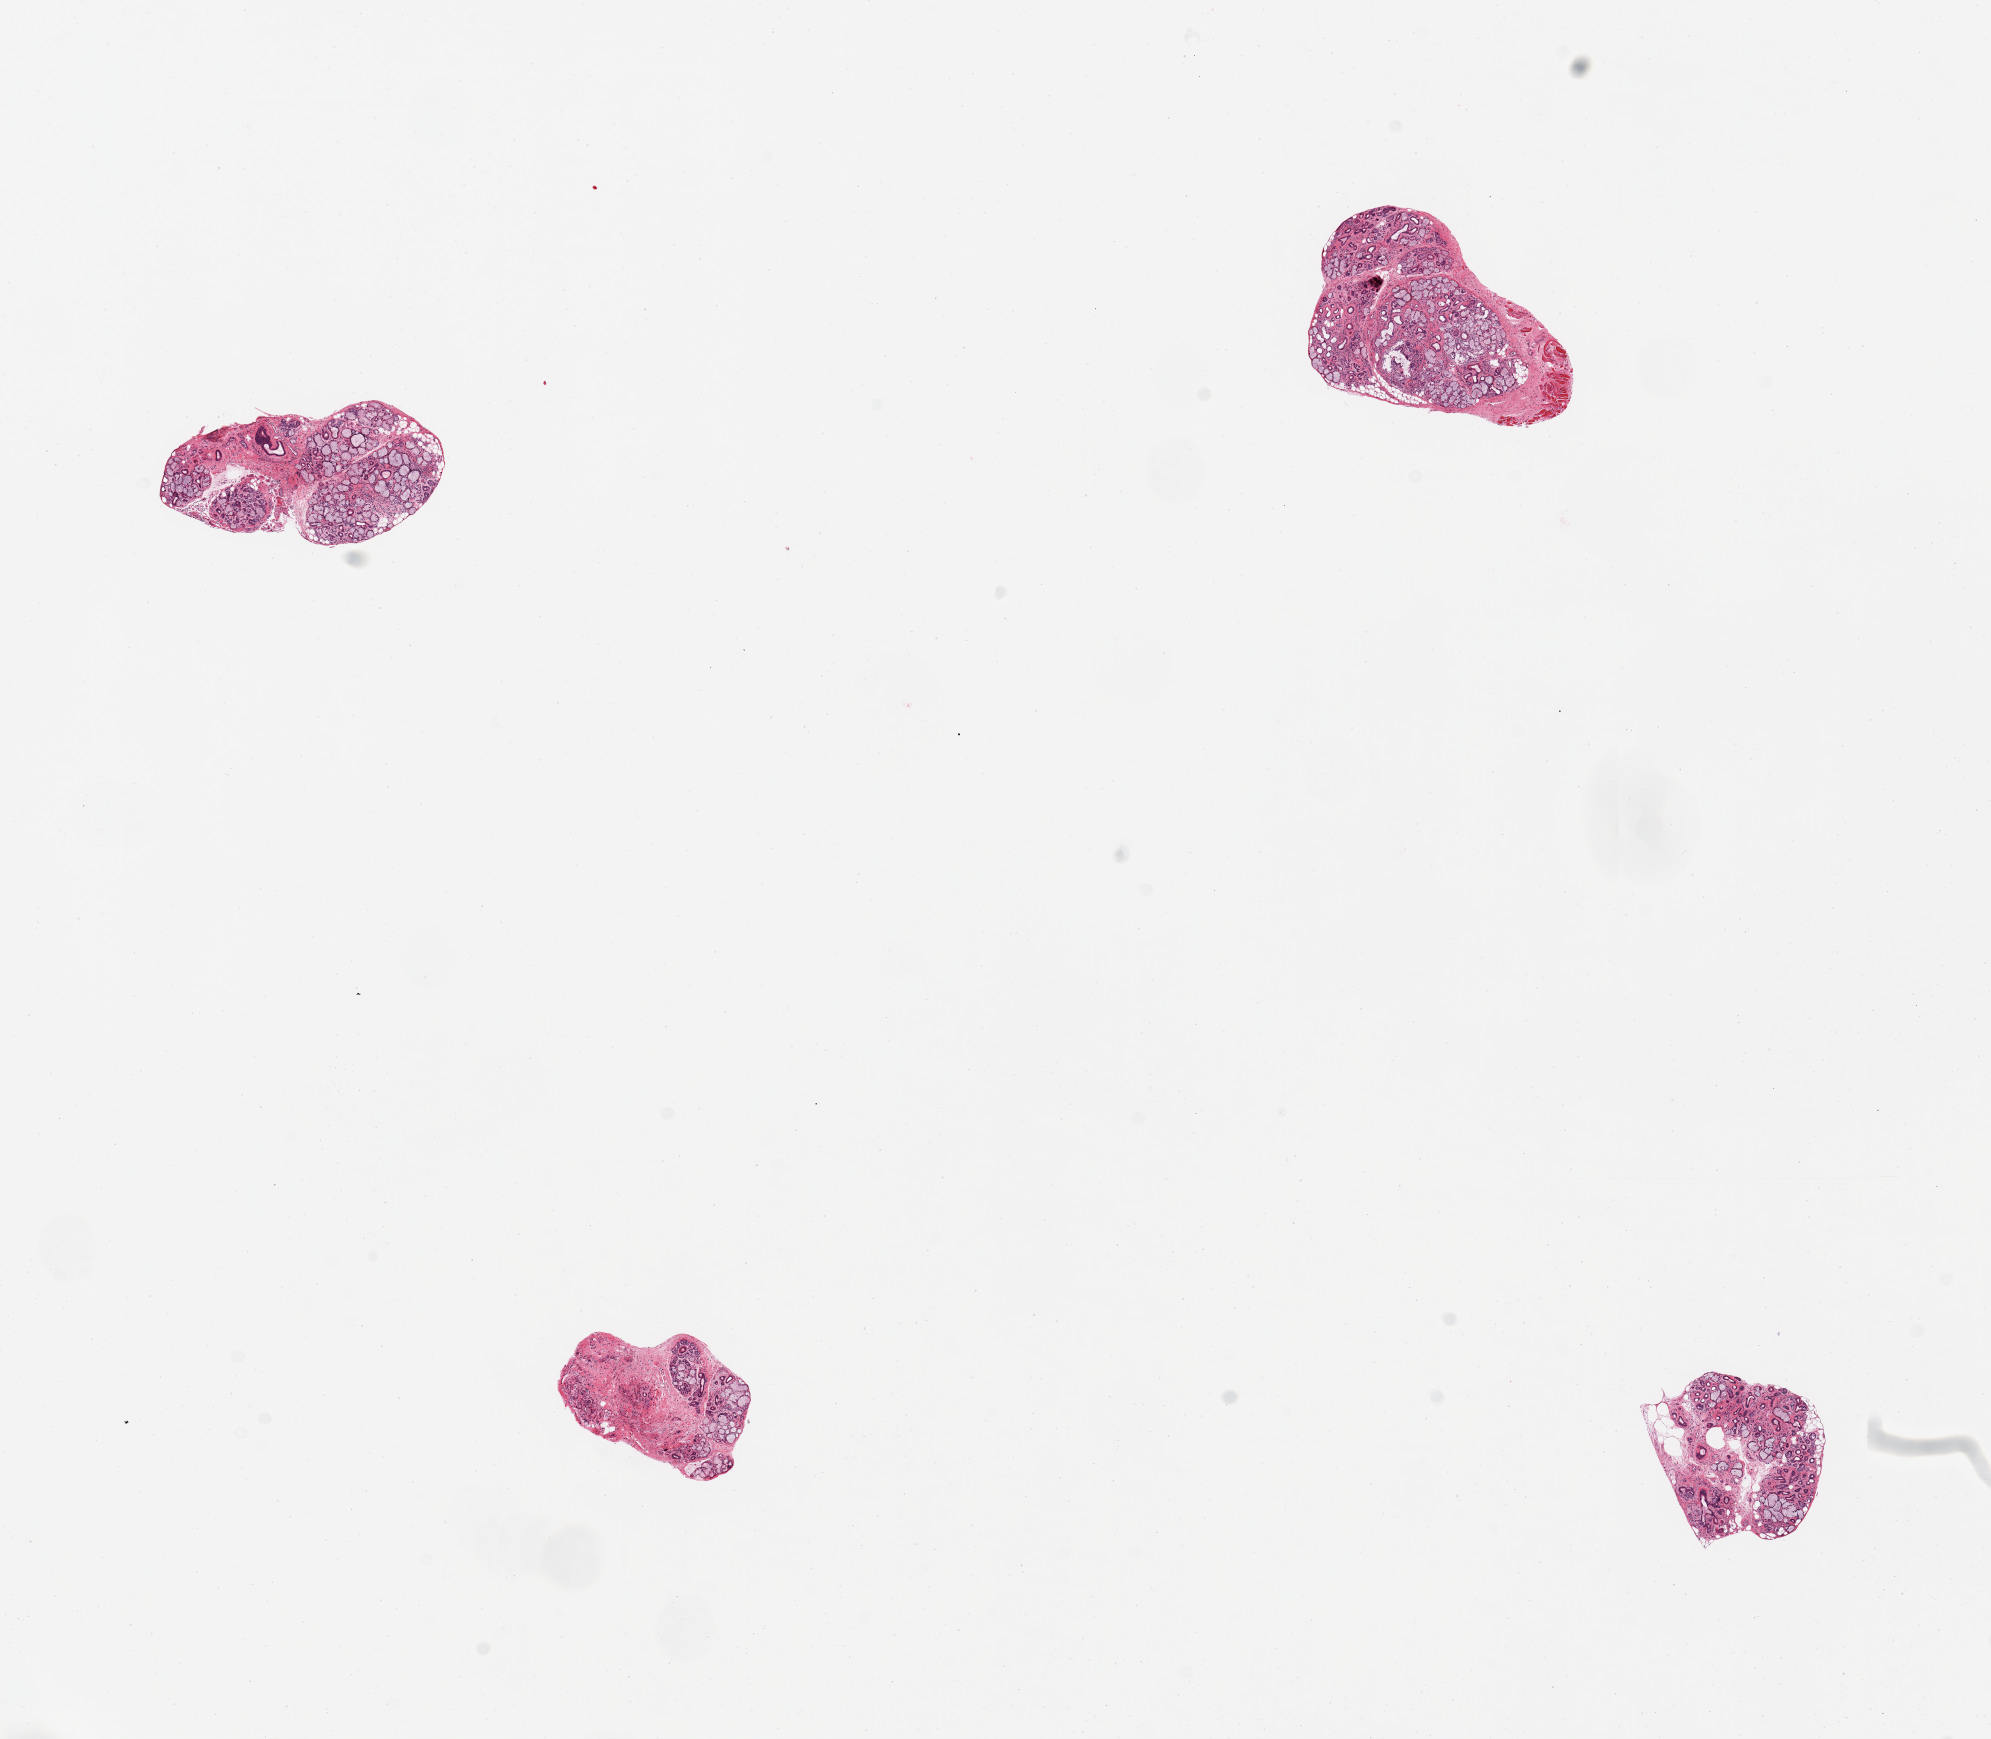
Whole-slide image, H&E stain — shown as a low-resolution overview of the whole scanned area (about 15.8 x 13.8 mm), PAXgene-fixed, paraffin-embedded tissue, sampled site (target tissue): minor salivary gland, tissue donor sample.
Pathologist's review note for this sample: 4 pieces, very good specimen, small attachment of stroma and skeletal muscle.